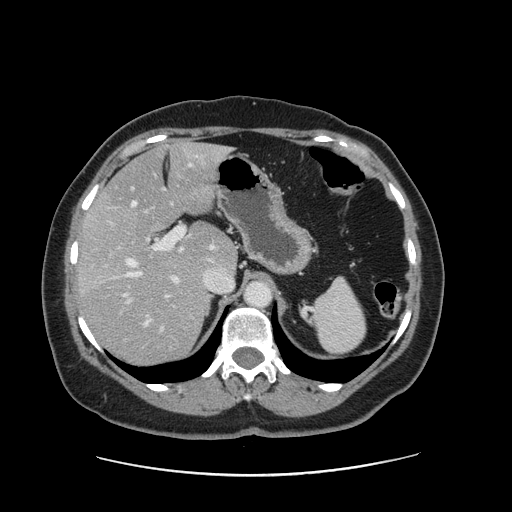
Contrast-enhanced abdominal CT, one axial slice. Position 100 of 161 along the scan axis. 120 kVp. Soft-tissue window (W 400 / L 40 HU). 2.5 mm slice thickness. 512 × 512 image matrix, field of view 398 × 398 mm. Female patient, age 62 years. From the clinical record (not read from this slice): diagnosis: colorectal cancer liver metastases, imaged before liver resection; multiple liver metastases: no; largest metastasis: 2.5 cm; disease in both lobes: no.
Annotated regions visible in this slice (expert manual segmentation):
- hepatic veins: box from (x=125, y=164) to (x=233, y=324) px
- liver: (x=79, y=144)–(x=236, y=363)
- planned liver remnant (the part of the liver to remain after resection): (x=103, y=143)–(x=236, y=270)
- portal vein (with intrahepatic branches): (x=125, y=227)–(x=191, y=332)